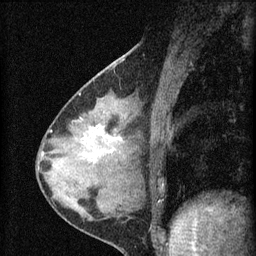
Breast MRI (dynamic contrast-enhanced), one sagittal slice. Position 25 of 60 along the scan axis. Dynamic contrast-enhanced series, image 2 of 4 at this slice position (ordered by acquisition). 1.5 T. TE 4.2 ms, TR 8.2 ms. 2 mm slice thickness. 256 × 256 image matrix. Patient: female, 37 years.
Structures marked on this image (semi-automatically segmented with operator editing):
- analysis volume of interest (the breast-tissue region the enhancement analysis was run in; not a lesion): box from (x=77, y=116) to (x=127, y=175) px
- tumour enhancement mask (voxels above the 70 % enhancement threshold inside the analysis volume of interest): (x=94, y=124)–(x=118, y=152)